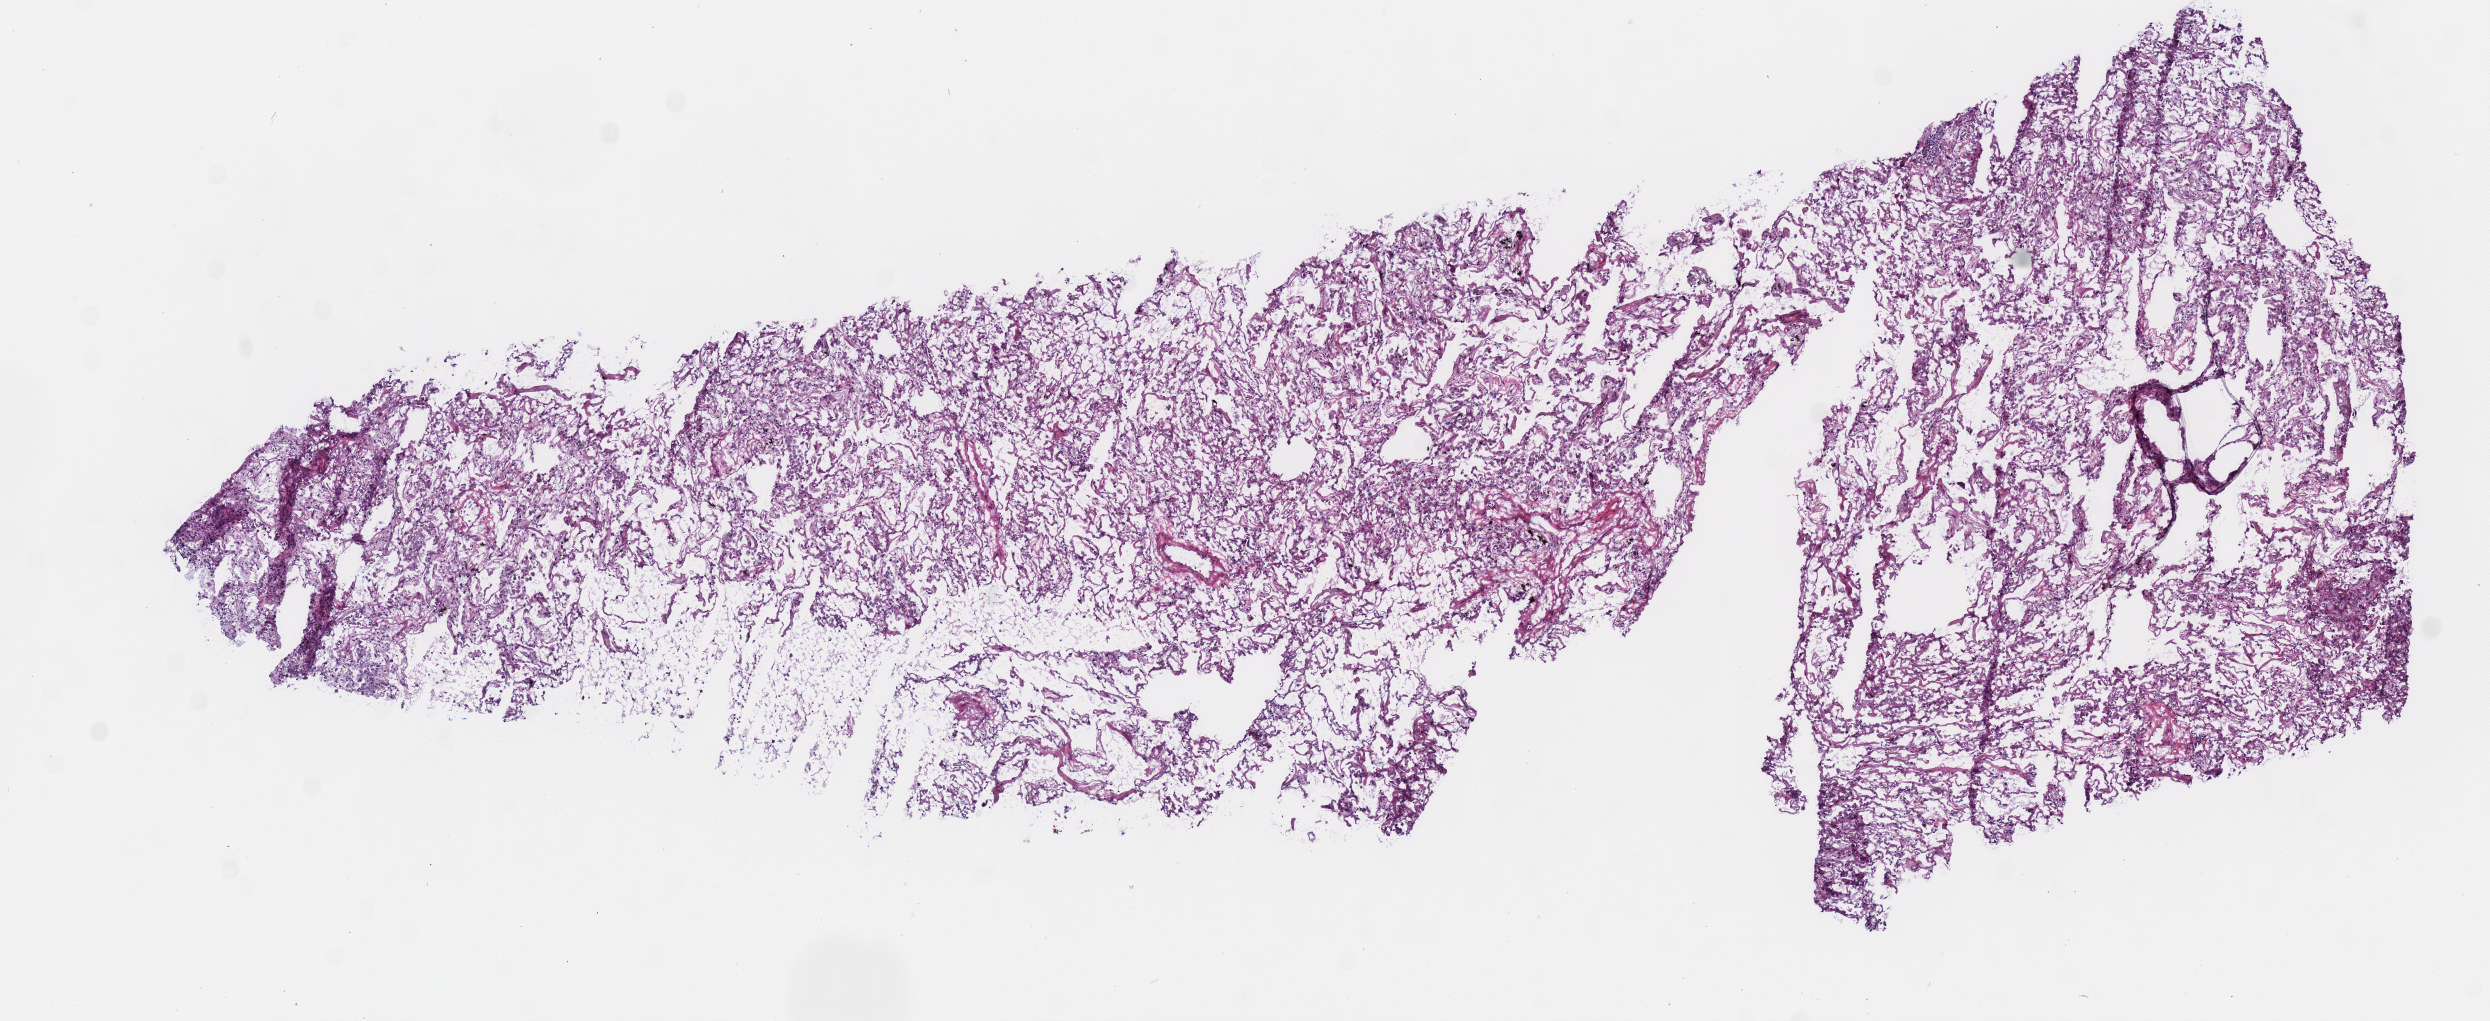
Whole-slide histology image, H&E, whole scanned area (about 9.8 x 4.0 mm) shown as a low-resolution overview, frozen section, solid tissue normal (non-tumour tissue) sample from the lung. Female, age 62 years at initial diagnosis.
This section: solid tissue normal (non-tumour) sample from the same patient. Patient diagnosis: Adenocarcinoma, NOS.